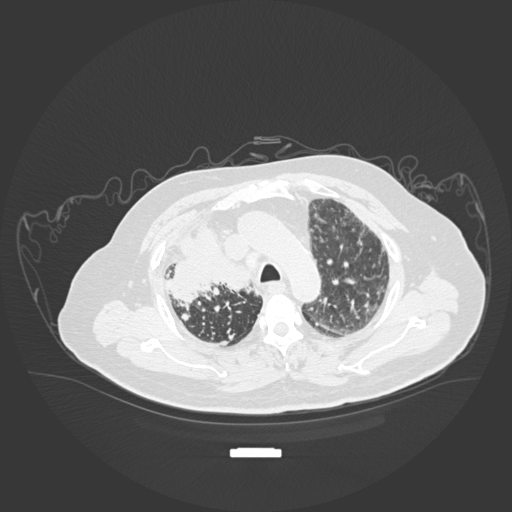
Chest CT, one axial slice. Position 138 of 201 along the scan axis. Reconstruction kernel B30f. Lung window (W 1500 / L -600 HU). 512 × 512 image matrix, field of view 500 × 500 mm. Male patient, age 69 years. From the clinical record (not read from this slice): clinical TNM (as recorded): T4 N3 M1.
Outlined on this slice (rectangle marked by the reading radiologist):
- lung tumour (recorded histology: adenocarcinoma): bounding box [x1, y1, x2, y2] px = [165, 218, 256, 307]